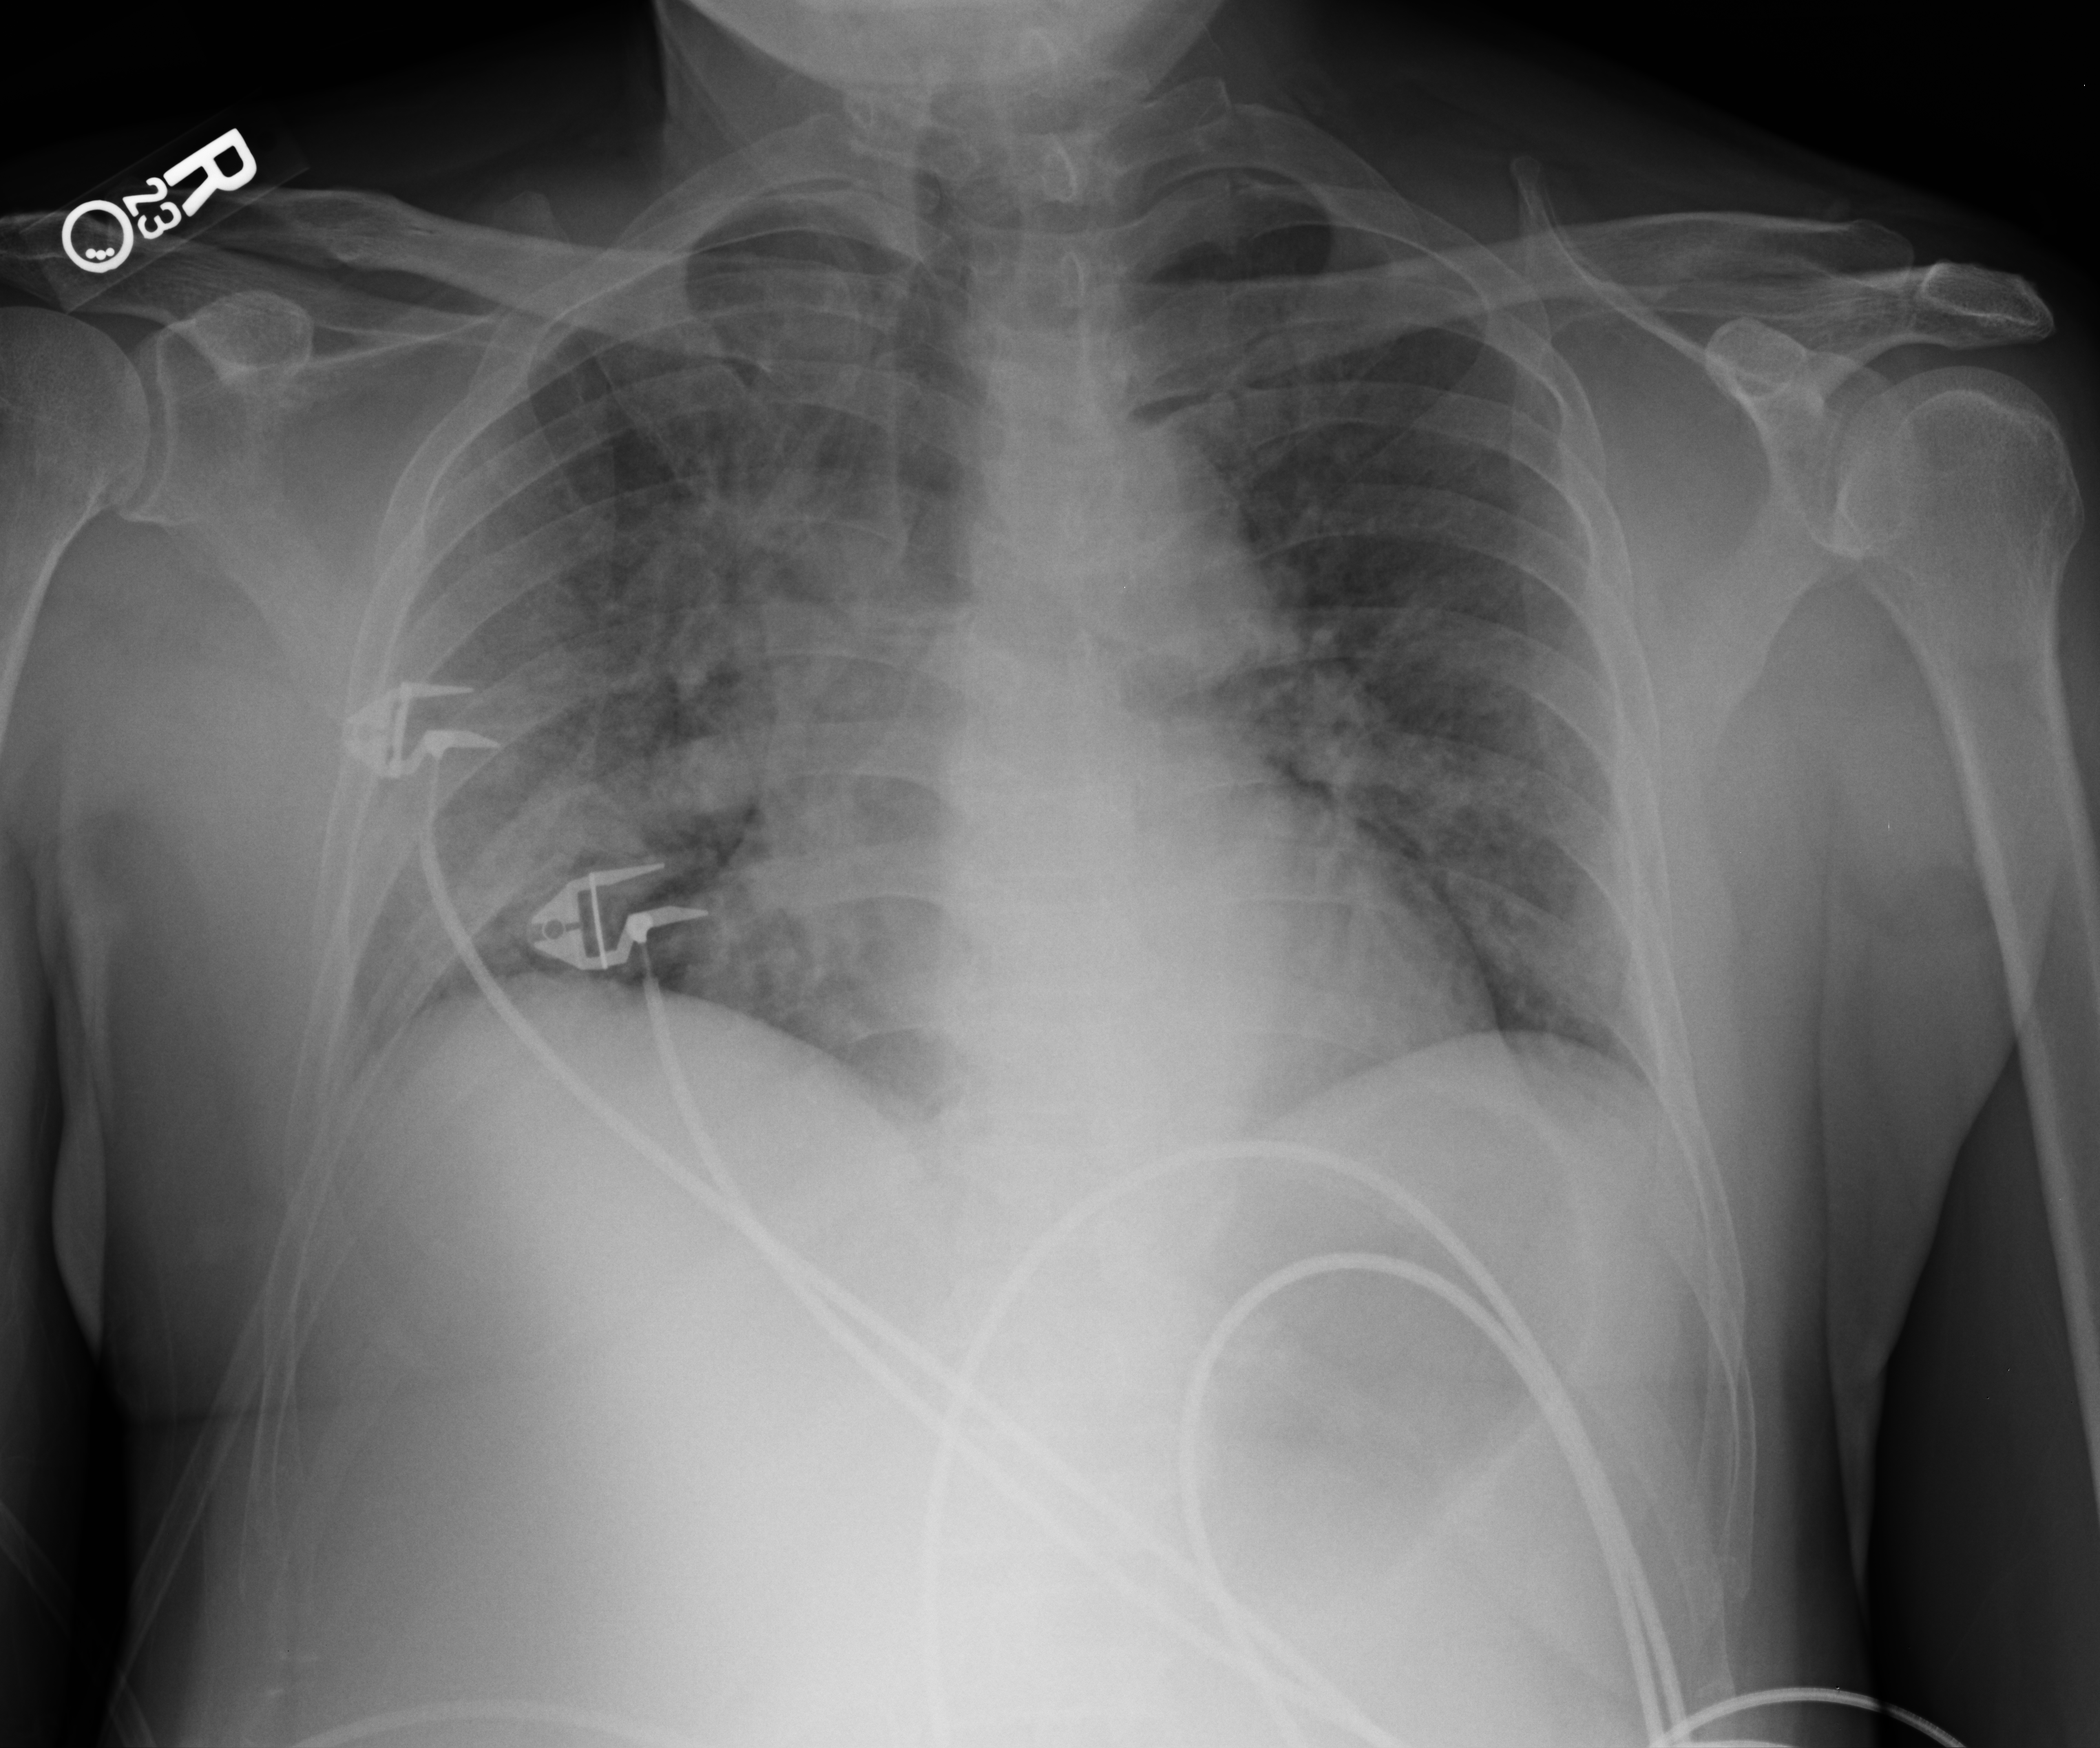
Bedside chest radiograph (computed radiography). Patient hospitalised with COVID-19; male, aged 60–74 years.
Admission-level facts for this patient (not findings on this image; timing relative to this image not recorded): diabetes (admission record): no.